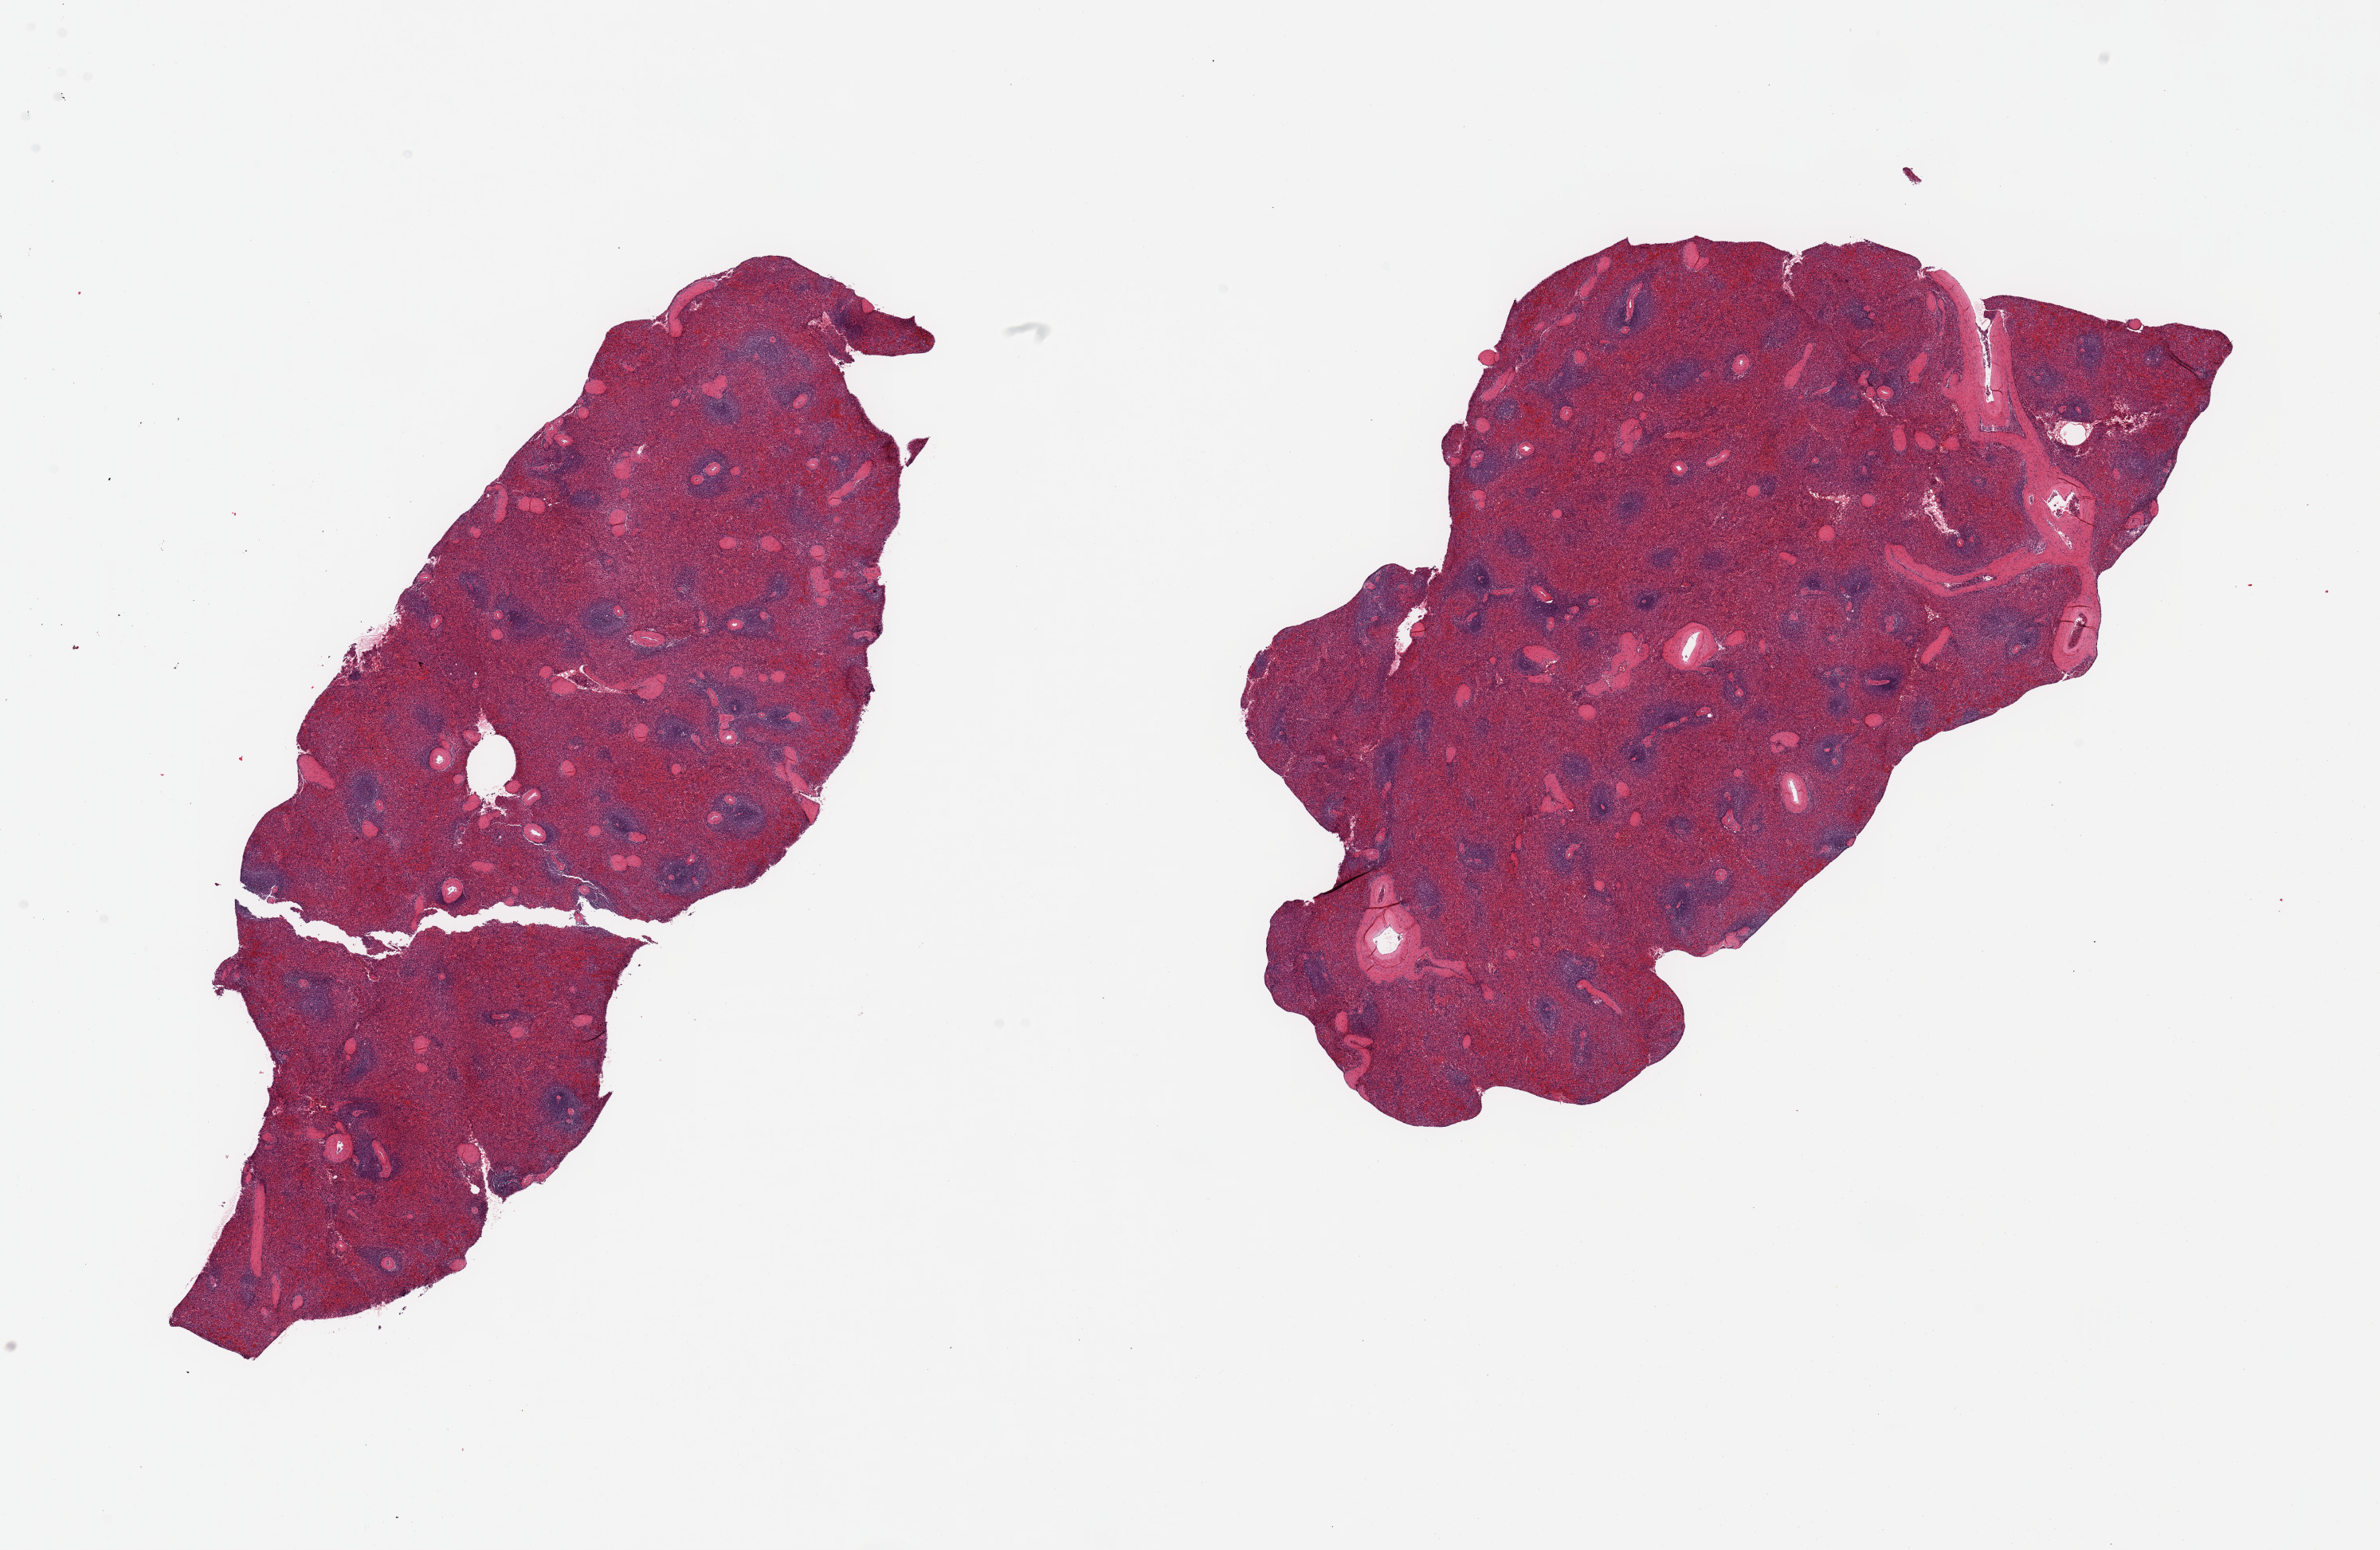
Hematoxylin and eosin (H&E) whole-slide image — low-resolution overview of the scanned area, about 23.6 x 15.4 mm (from a 20x scan), PAXgene-fixed paraffin-embedded (PFPE) section, sampled site (target tissue): spleen, tissue donor sample. Male donor.
Pathologist's review note for this sample: 2 pieces; moderate congestion.